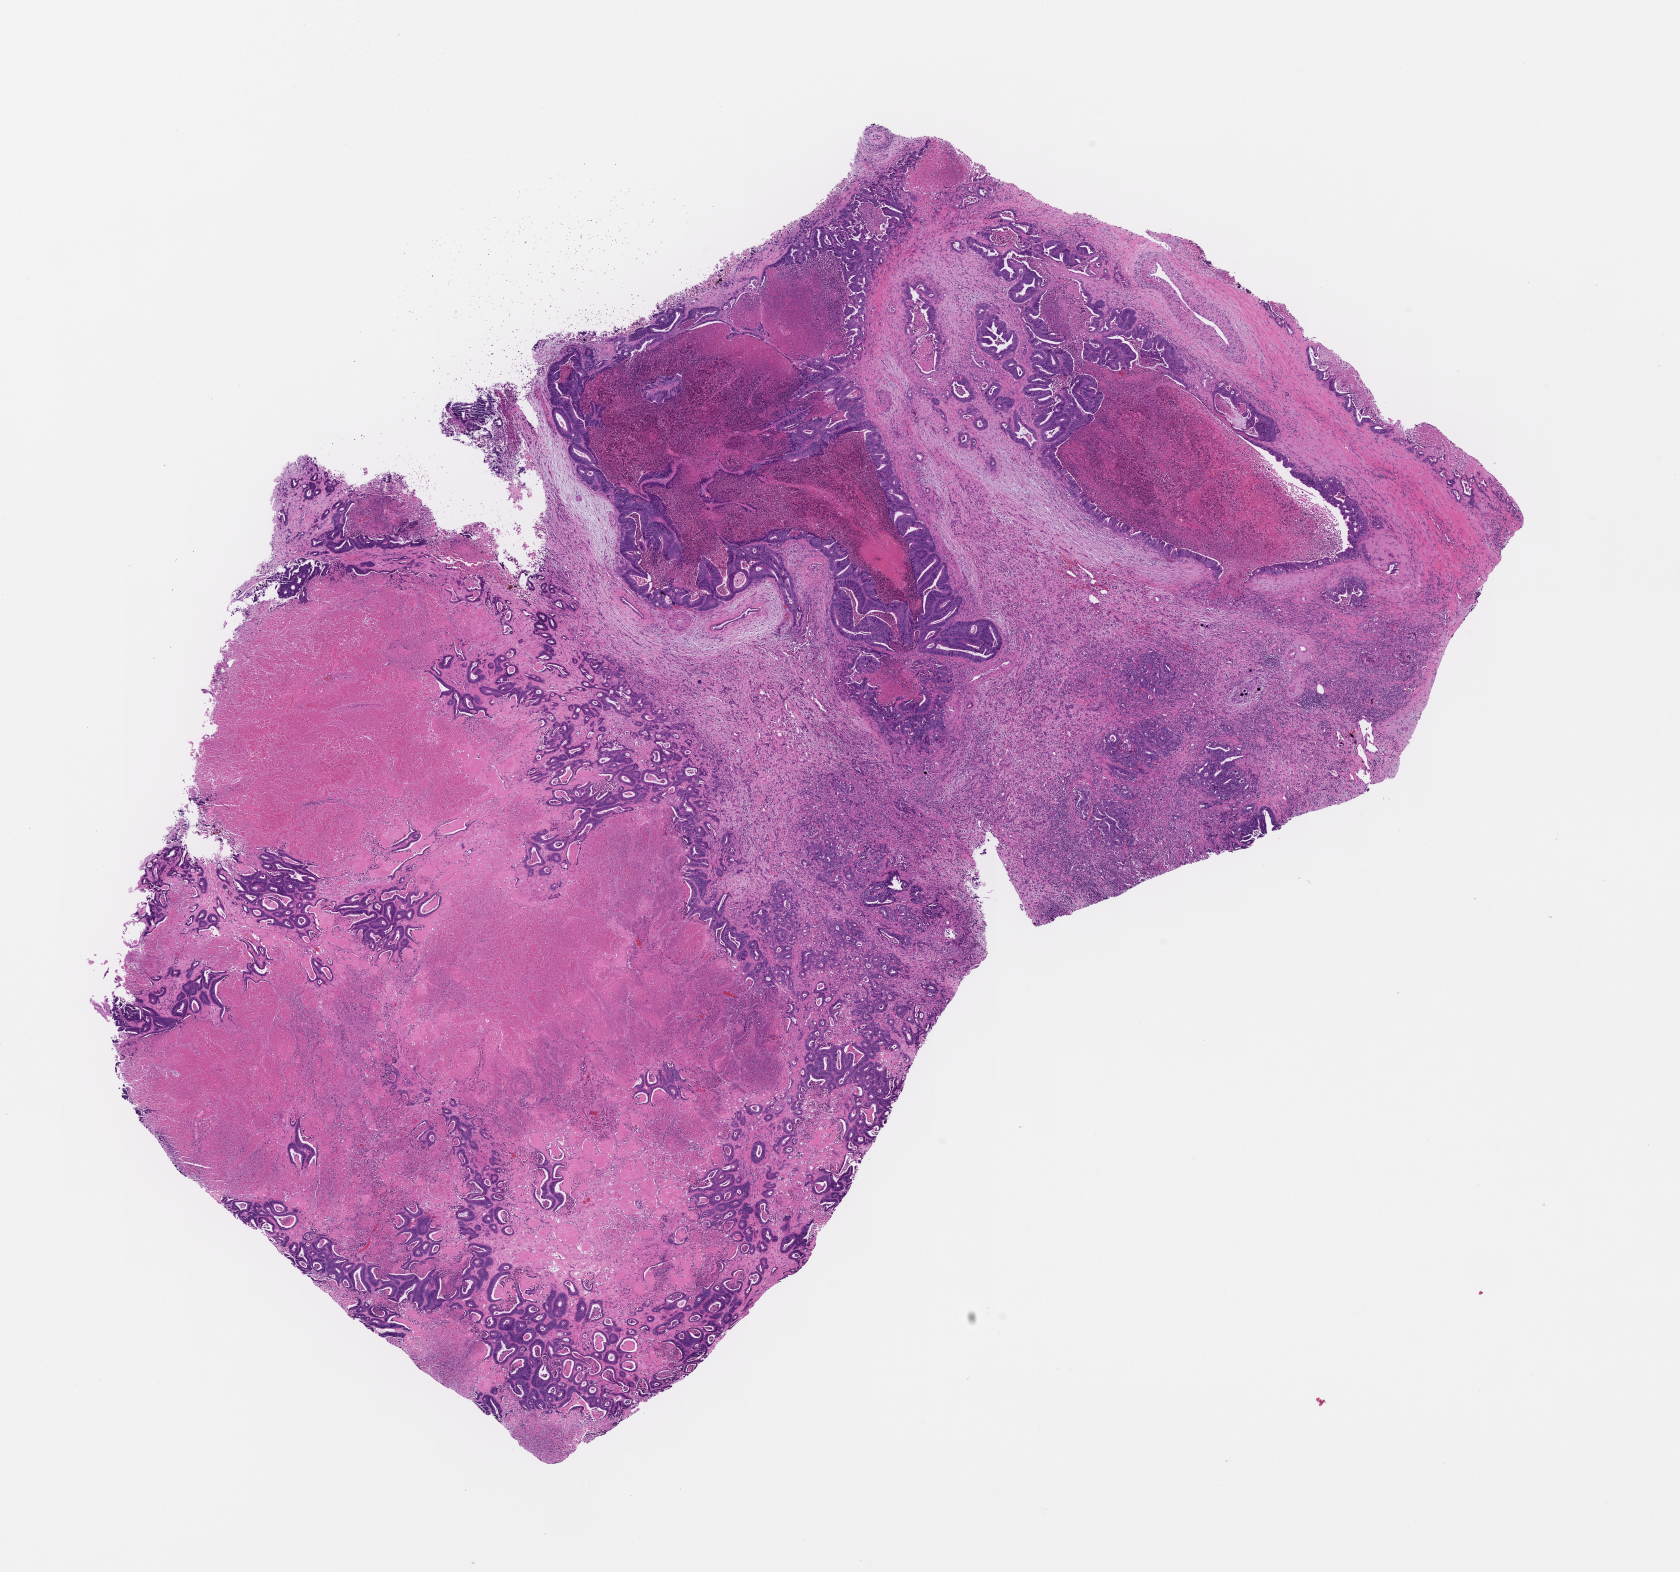
Hematoxylin and eosin (H&E) whole-slide image — a low-resolution overview of the entire scanned area, about 13.6 x 12.7 mm. FFPE section. Patient: female.
This section: metastatic tumor tissue. Primary diagnosis of the patient: Colorectal Carcinoma.